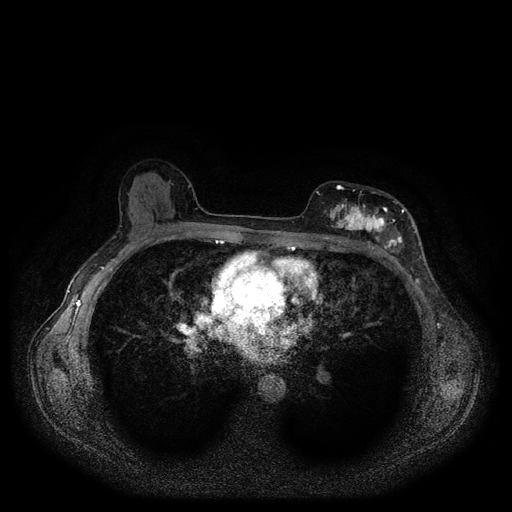
Breast MRI (dynamic contrast-enhanced, multi-phase), one axial slice; position 61 of 116 along the scan axis; dynamic contrast-enhanced series, time point 2 of 5 at this slice position (early post-contrast); 1.5 T; TE 2.6 ms, TR 5.3 ms; 2 mm slice thickness; 512 × 512 image matrix. Female patient, age 51 years.
Structures marked on this image (semi-automatically segmented with operator editing):
- breast lesion (labelled 'tumour' in the annotation; benign lesions carry a separate 'benign' label): box from (x=328, y=196) to (x=407, y=254) px